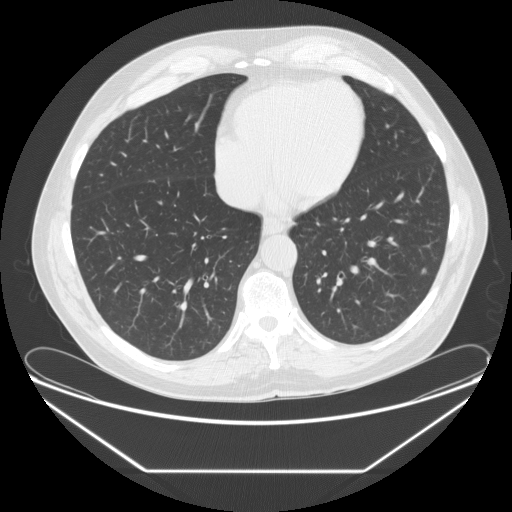
Axial slice from a low-dose chest CT screening exam. Baseline screening round. Lung window (W 1500 / L -600 HU). 2.5 mm slice thickness. Standard (soft-tissue) reconstruction kernel (STANDARD). Slice 172 of 261 in the series. Male, age 67 years at enrolment. Current smoker at enrolment.
Lesion marked by an expert reader, box from (x=414, y=258) to (x=435, y=282) px. Screening reader's record for this exam (one nodule recorded; not confirmed to be the boxed lesion): non-calcified nodule or mass ≥4 mm, left lower lobe, 4 × 4 mm, poorly defined margins, soft tissue attenuation. Official screen result: positive, change unspecified: nodule(s) >= 4 mm or enlarging nodule(s), mass(es), or other non-specific abnormalities suspicious for lung cancer.